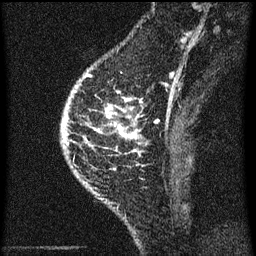
Breast MRI (dynamic contrast-enhanced), one sagittal slice. Position 19 of 60 along the scan axis. Dynamic contrast-enhanced series, image 2 of 3 at this slice position (ordered by acquisition). 1.5 T. TE 4.2 ms, TR 8 ms. 2 mm slice thickness. 256 × 256 image matrix, field of view 180 × 180 mm. Patient: female, 46 years.
Outlined on this slice (semi-automatically segmented with operator editing):
- analysis volume of interest (the breast-tissue region the enhancement analysis was run in; not a lesion): bounding box <90,68,145,195> (left, top, right, bottom; pixels)
- tumour enhancement mask (voxels above the 70 % enhancement threshold inside the analysis volume of interest): <93,92,142,153>